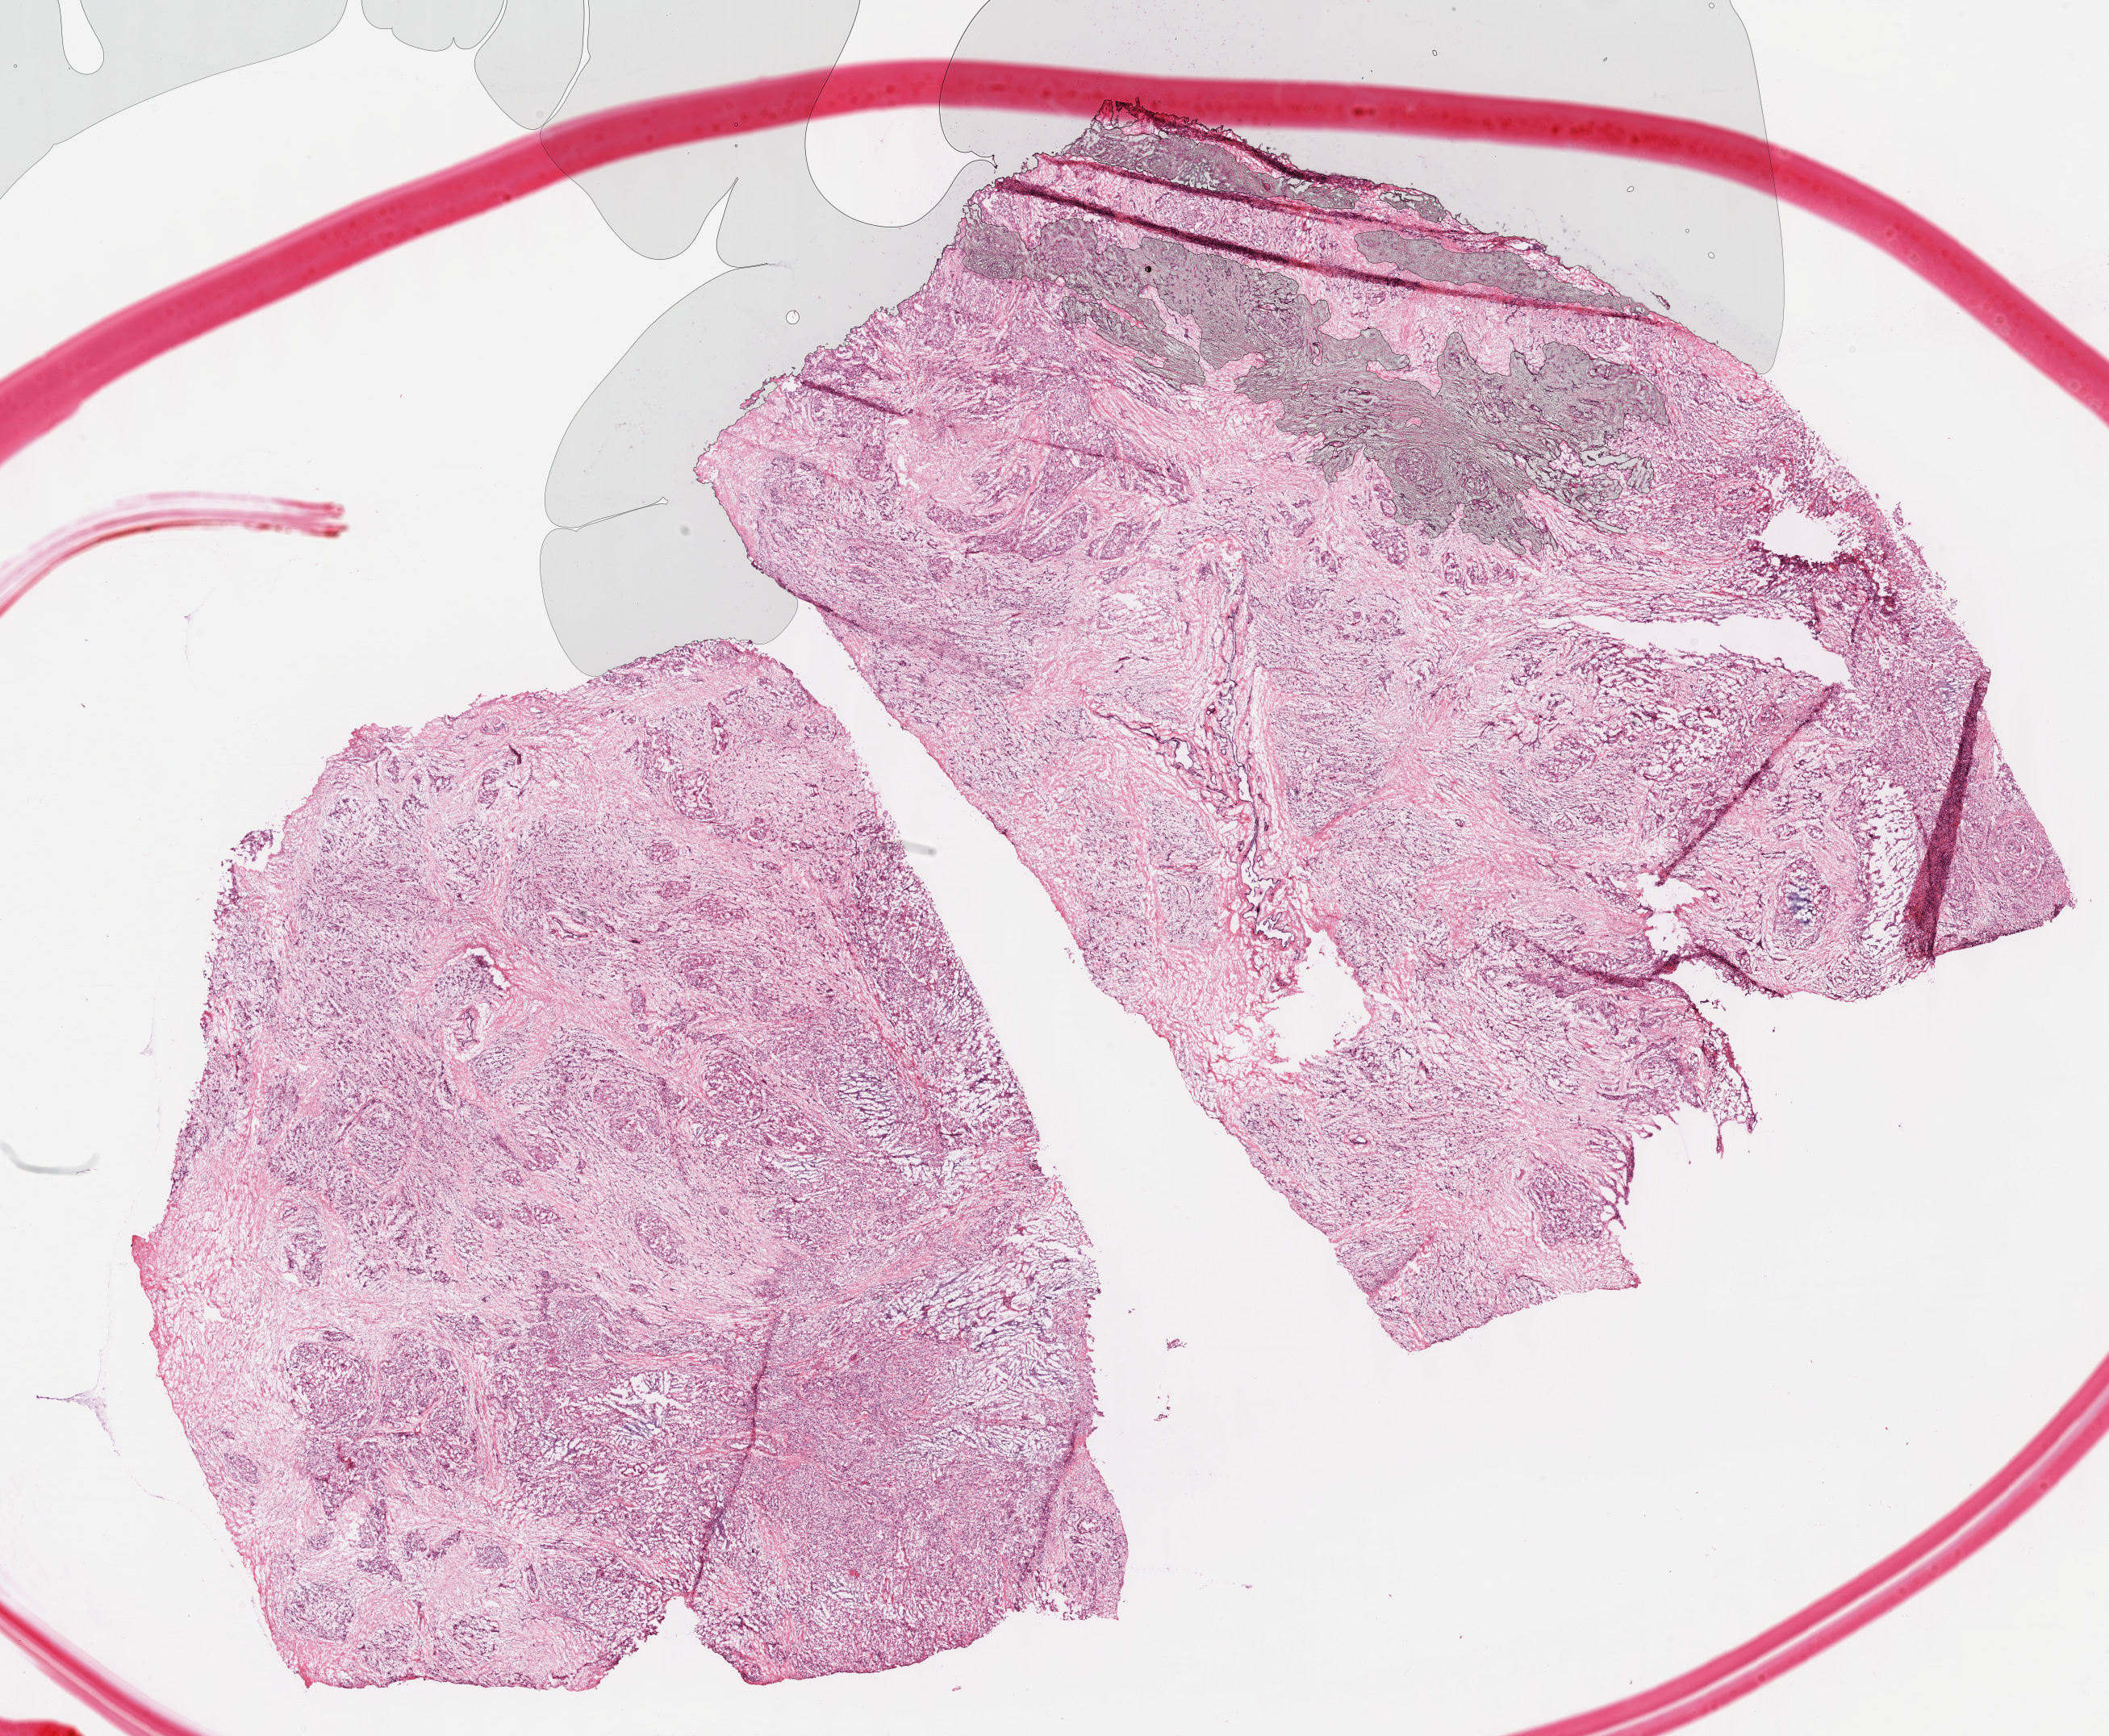
Digitized H&E tissue section (whole slide), low-resolution overview of the scanned area, about 21.1 x 17.4 mm, formalin-fixed paraffin-embedded (FFPE) diagnostic section, pancreas, primary tumour sample. Patient: male, age at initial diagnosis 49 years.
Pathologic diagnosis: Infiltrating duct carcinoma, NOS (head of pancreas).